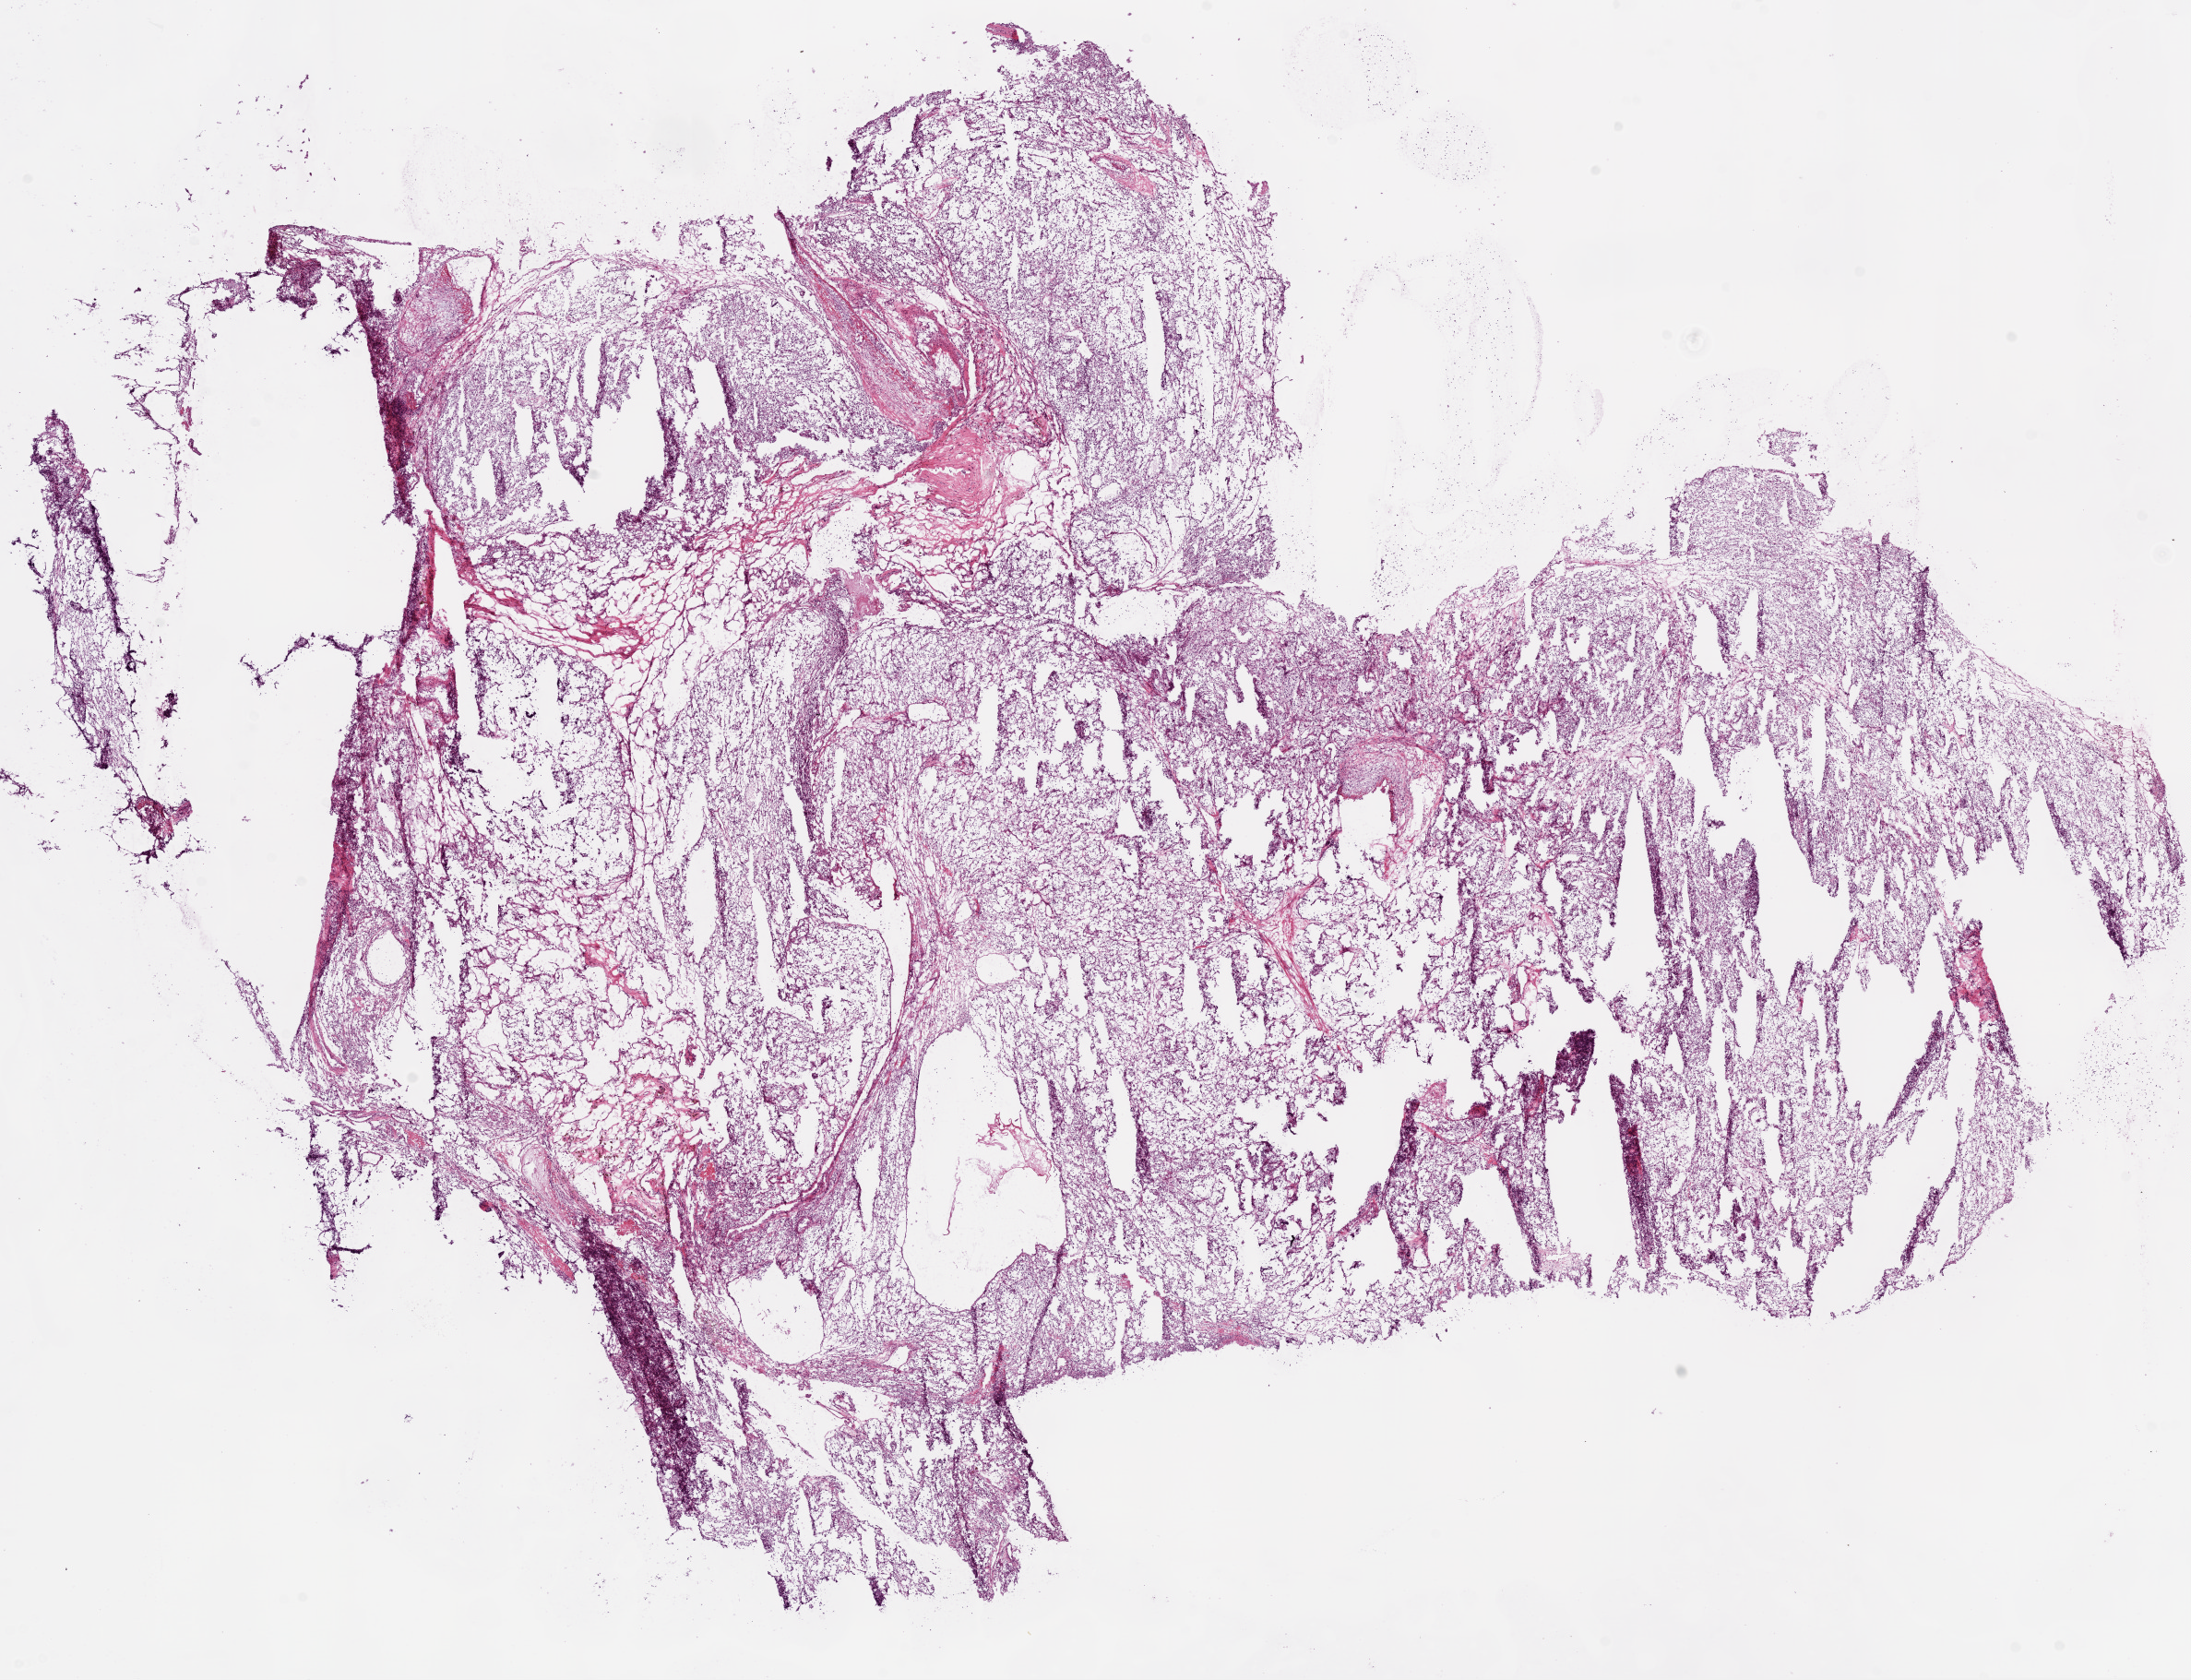
H&E-stained whole-slide image, whole scanned area (about 19.1 x 14.6 mm, slide scanned at 20x) shown as a low-resolution overview. Frozen section from the top of the tissue portion. Kidney, primary tumour sample. Female, age 47 years at initial diagnosis. Histologic grade: G2 (moderately differentiated). Pathologist review of this section (percent, as recorded): tumour cells 90%, tumour nuclei 80%, normal cells 0%, stromal cells 10%, necrosis 0%.
Diagnosis: Clear cell adenocarcinoma, NOS. AJCC pathologic stage: I (6th edition).